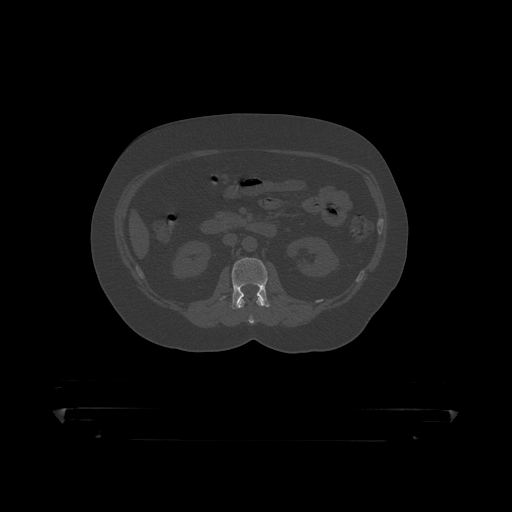
CT including the spine, one axial slice; position 126 of 390 along the scan axis; 120 kVp; bone window (W 1800 / L 400 HU); 1.25 mm slice thickness; 512 × 512 image matrix. Patient: male, 60 years. From the clinical record (not read from this slice): primary cancer: prostate.
Structures marked on this image (semi-automatic segmentation, software-assisted and operator-edited):
- L1 vertebra: bounding box (x1, y1, x2, y2) in pixels: (239, 299, 264, 319)
- L2 vertebra: (232, 258, 270, 310)